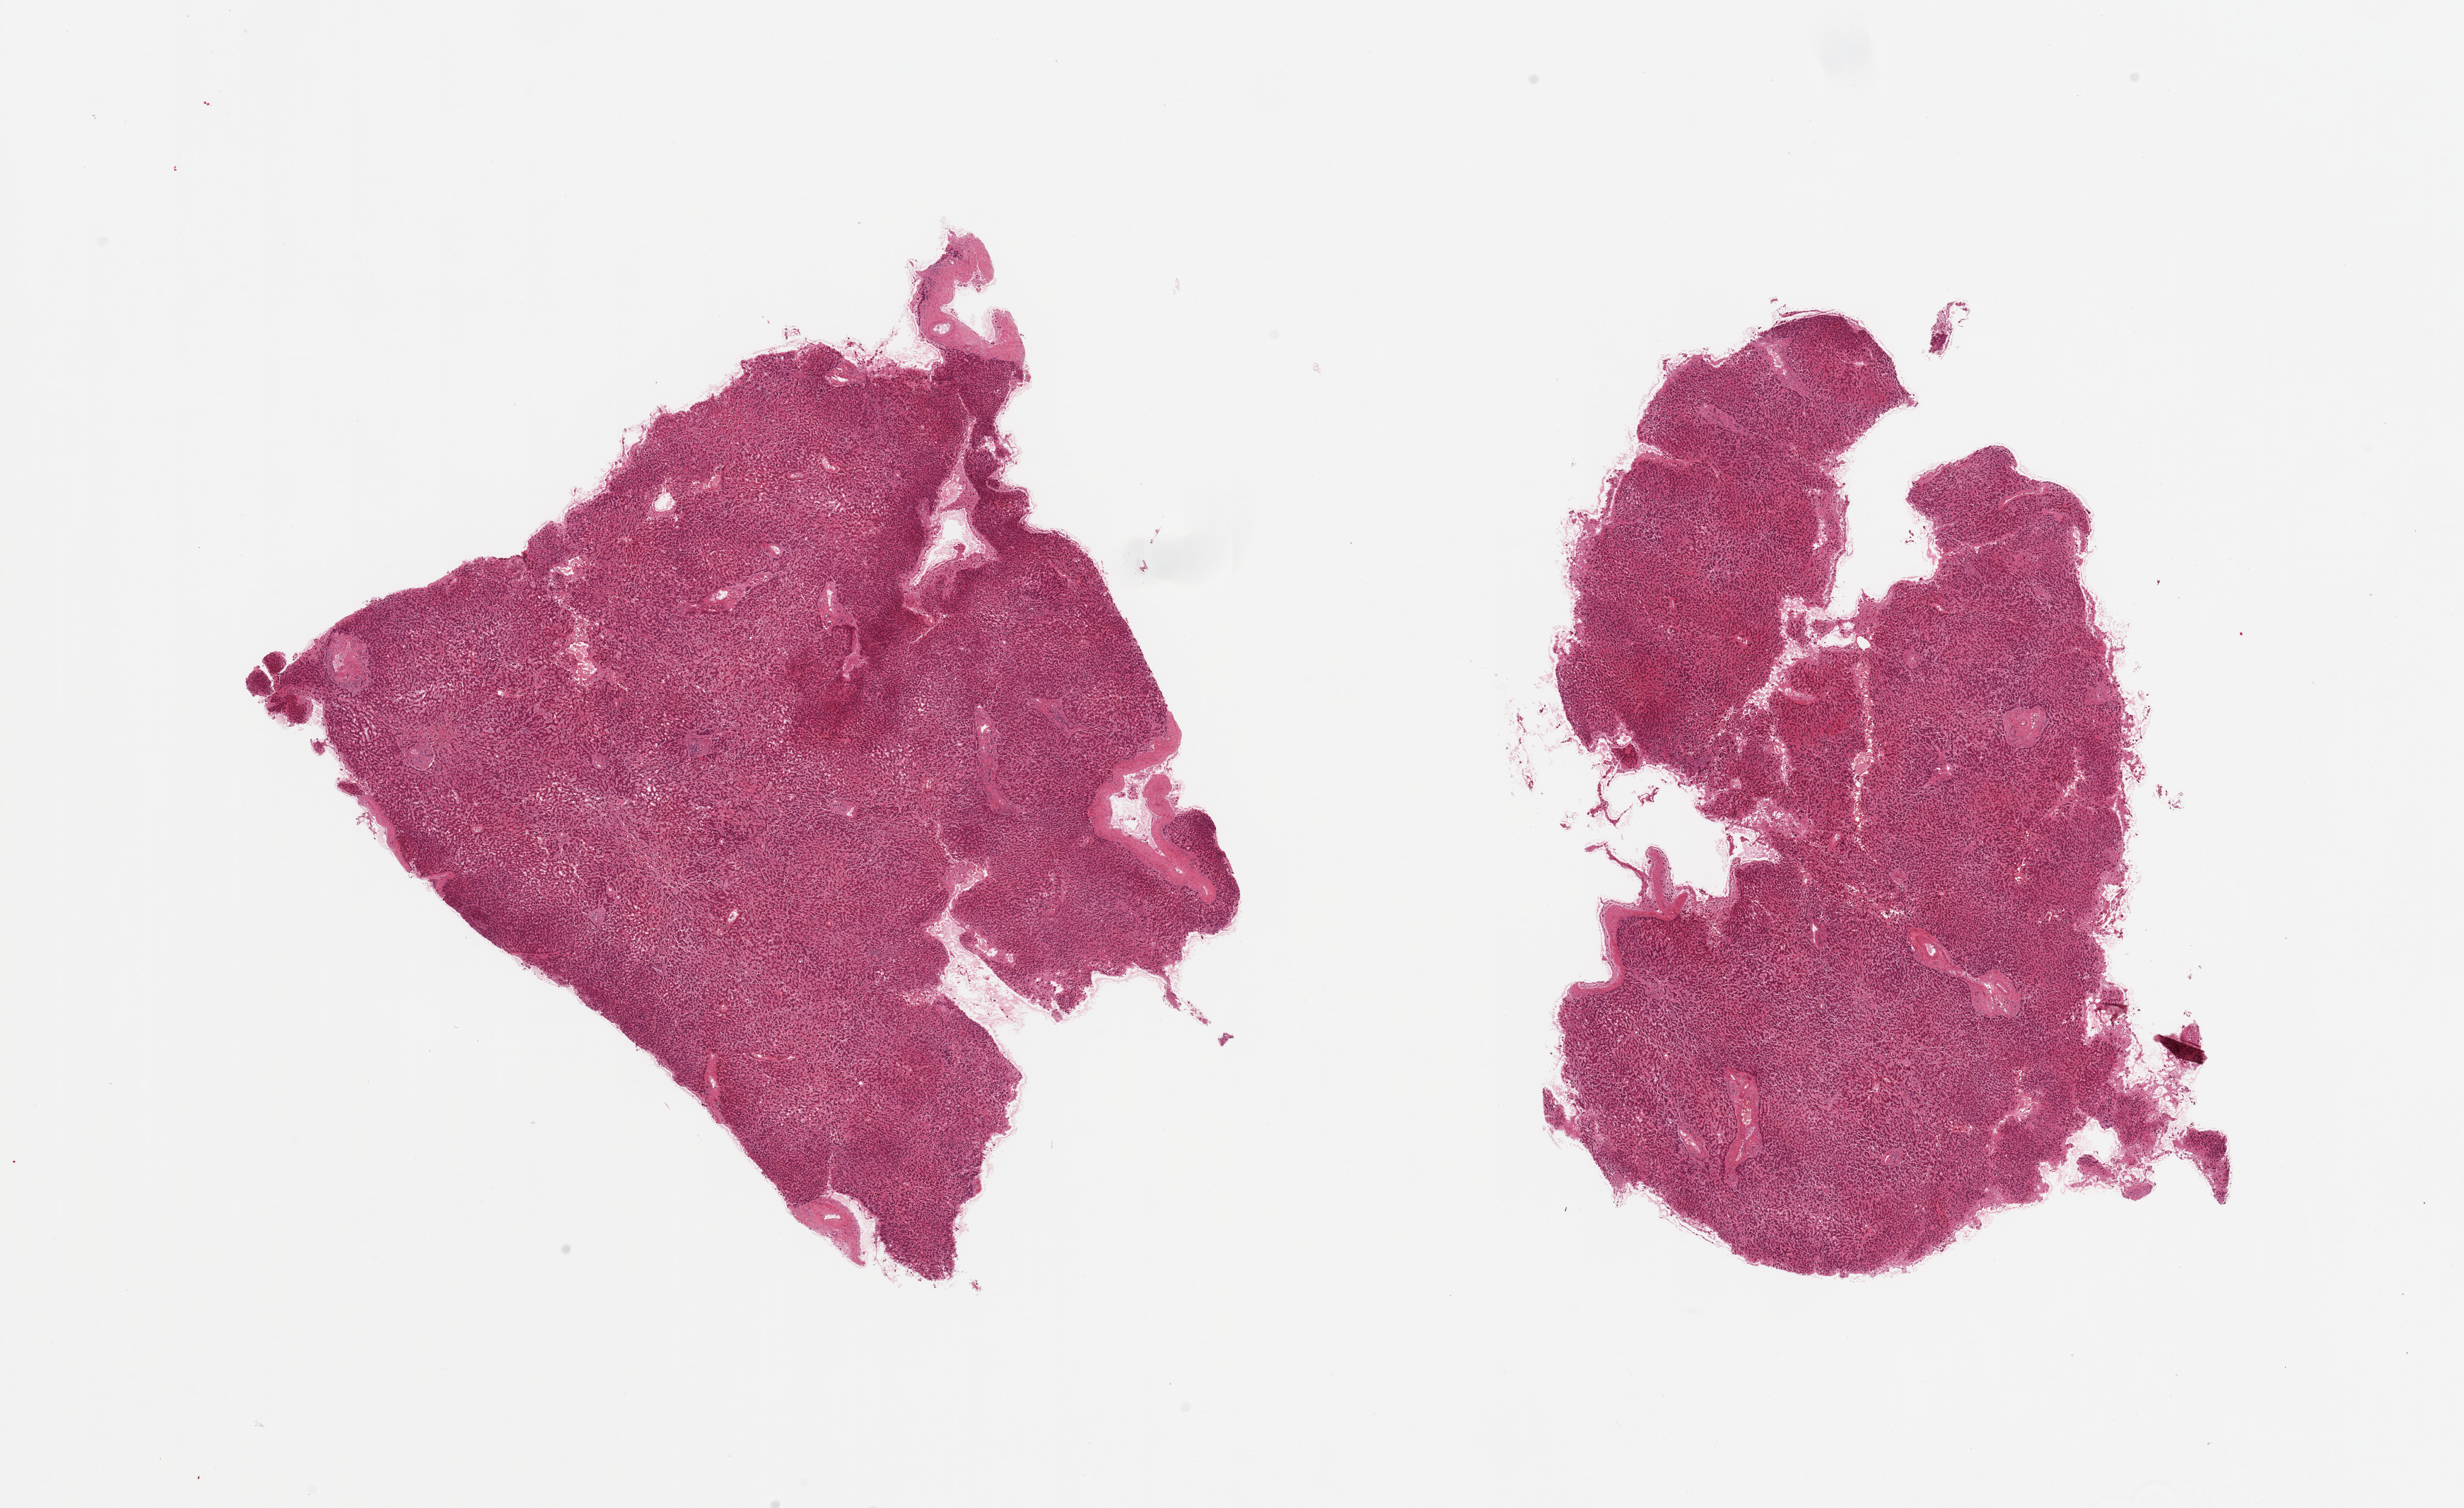
H&E whole-slide image — shown as a low-resolution overview of the whole scanned area (about 27.6 x 16.9 mm, from a 20x scan); PAXgene-fixed, paraffin-embedded tissue; sampled site (target tissue): liver; donor tissue sample. Male donor.
Pathologist's review note for this sample: 2 pieces; portal fibrosis, congestion.